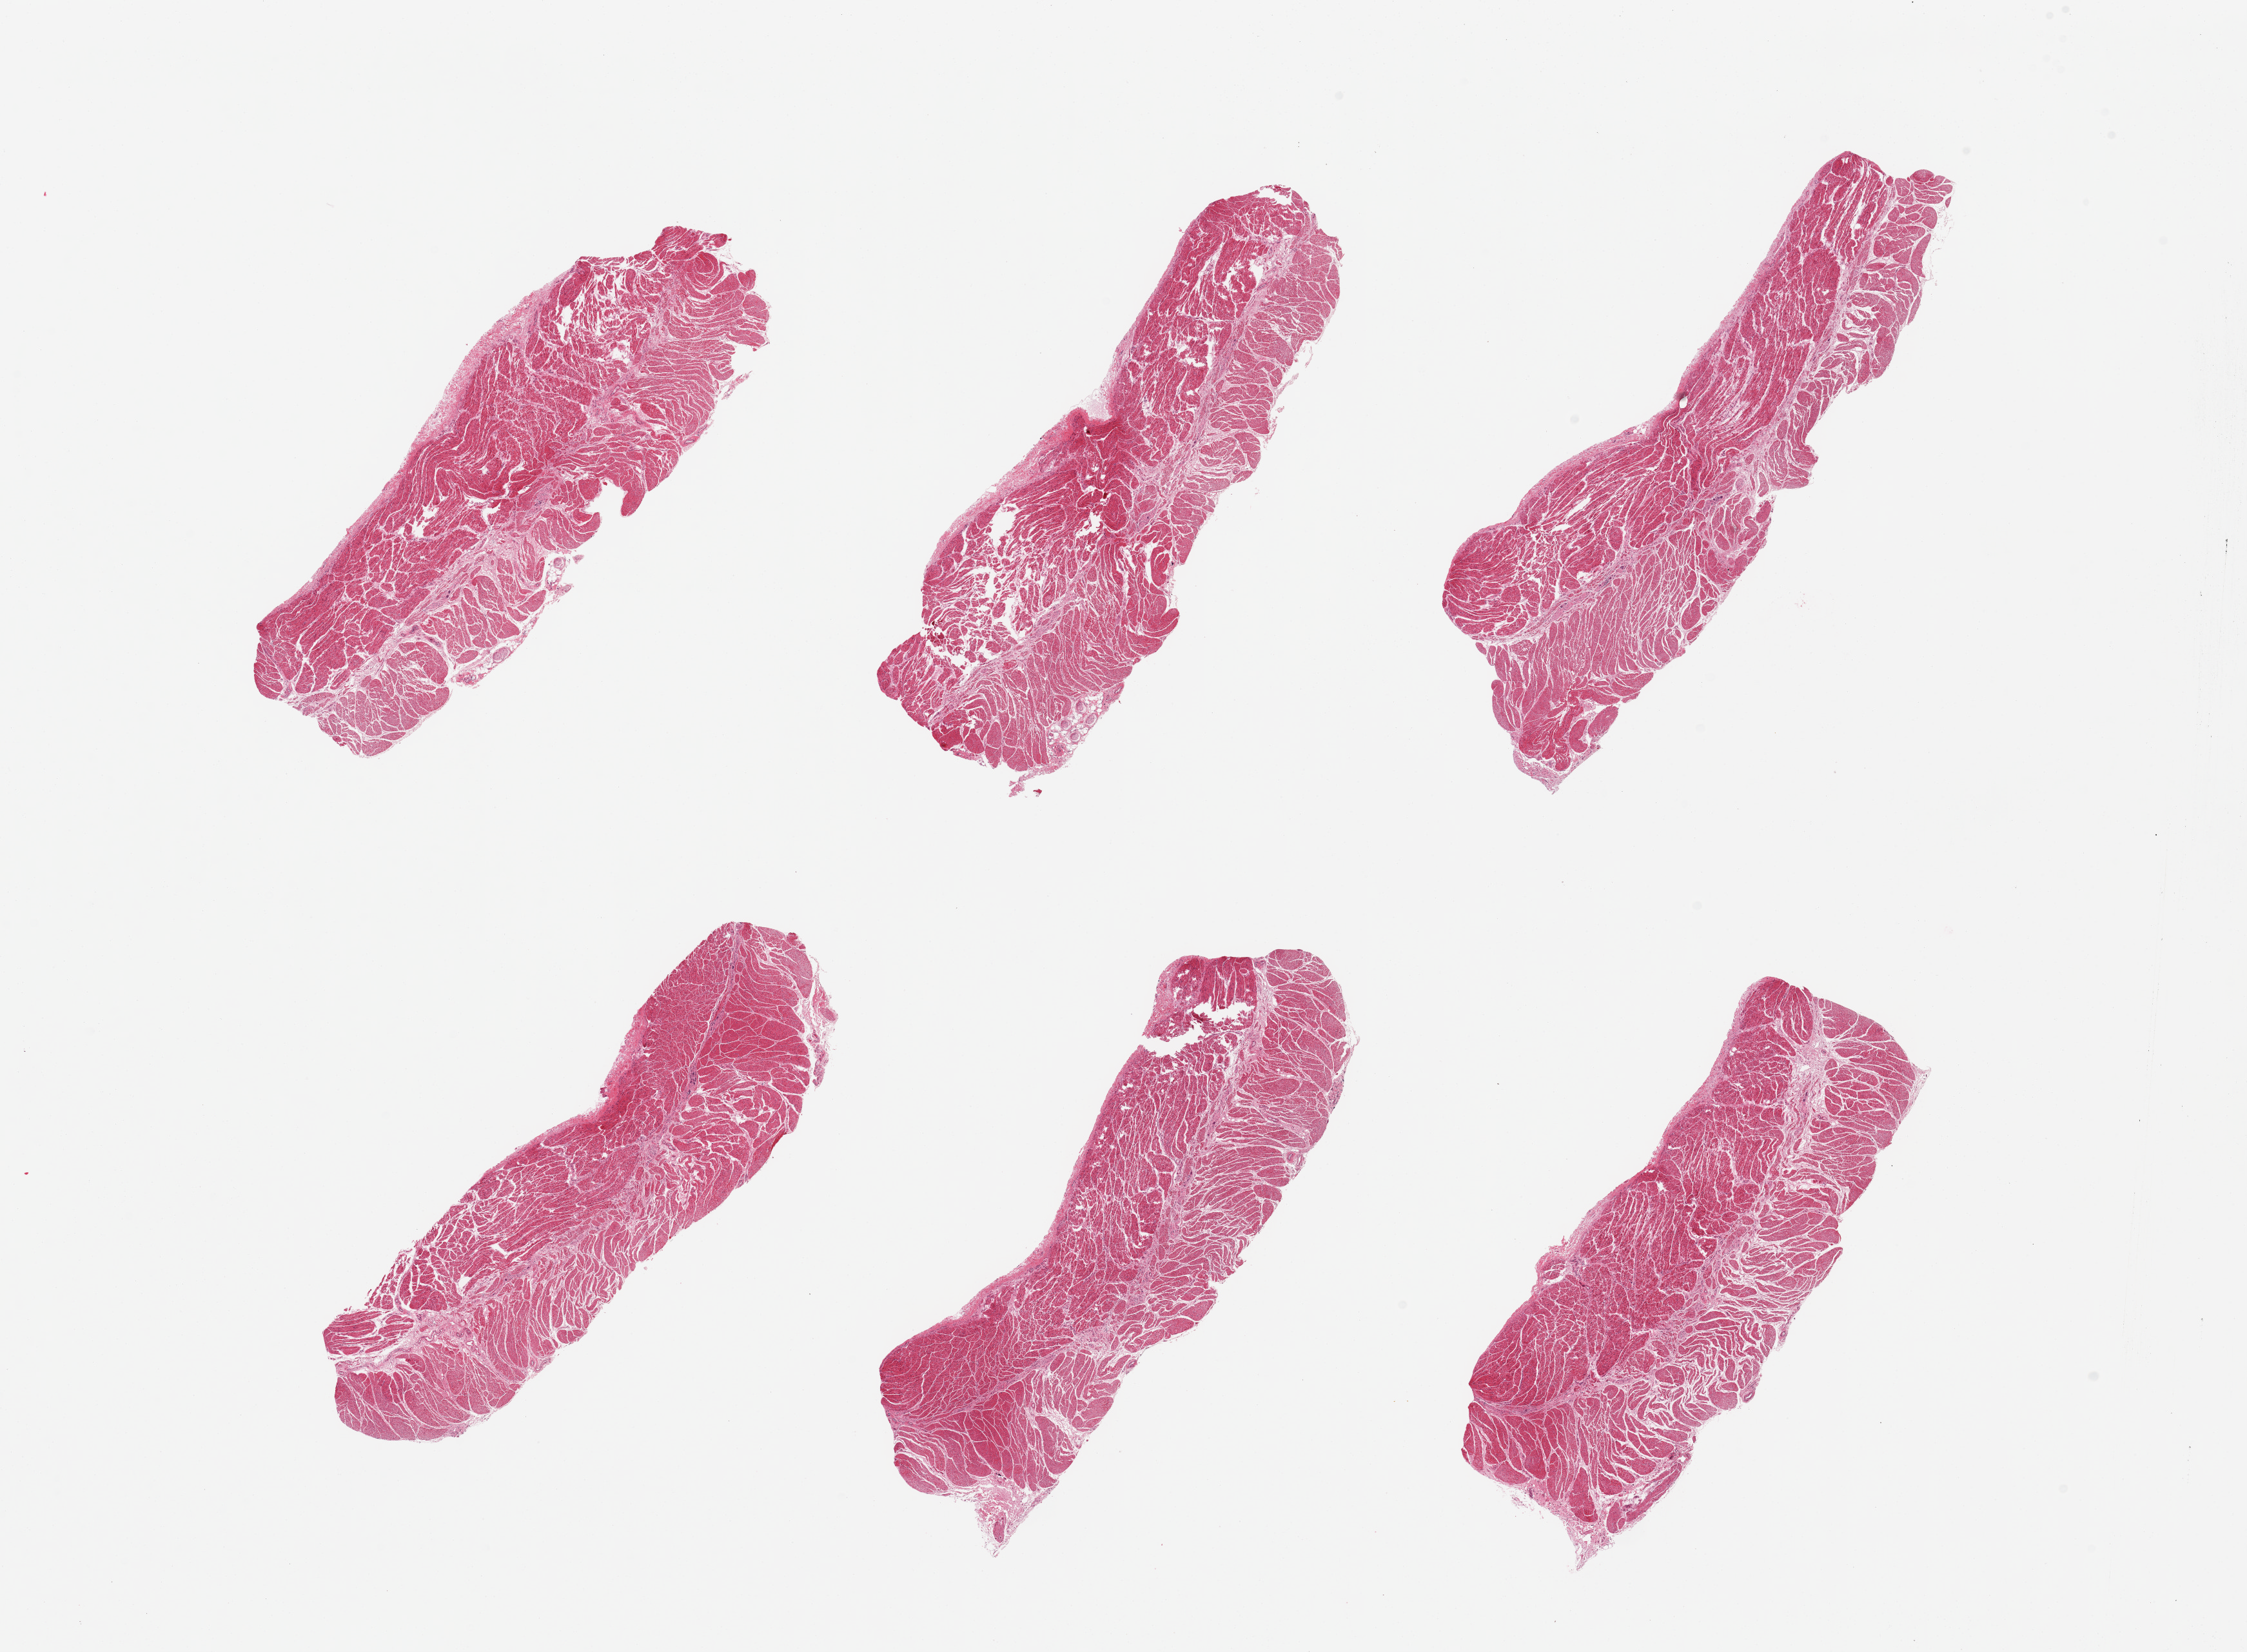
Whole-slide image, haematoxylin and eosin stain, a low-resolution overview of the entire scanned area, about 27.6 x 20.3 mm; PAXgene-fixed, paraffin-embedded tissue; sampled site (target tissue): esophageal muscle; donor tissue sample.
• pathologist's review note for this sample: 6 pieces; well dissected